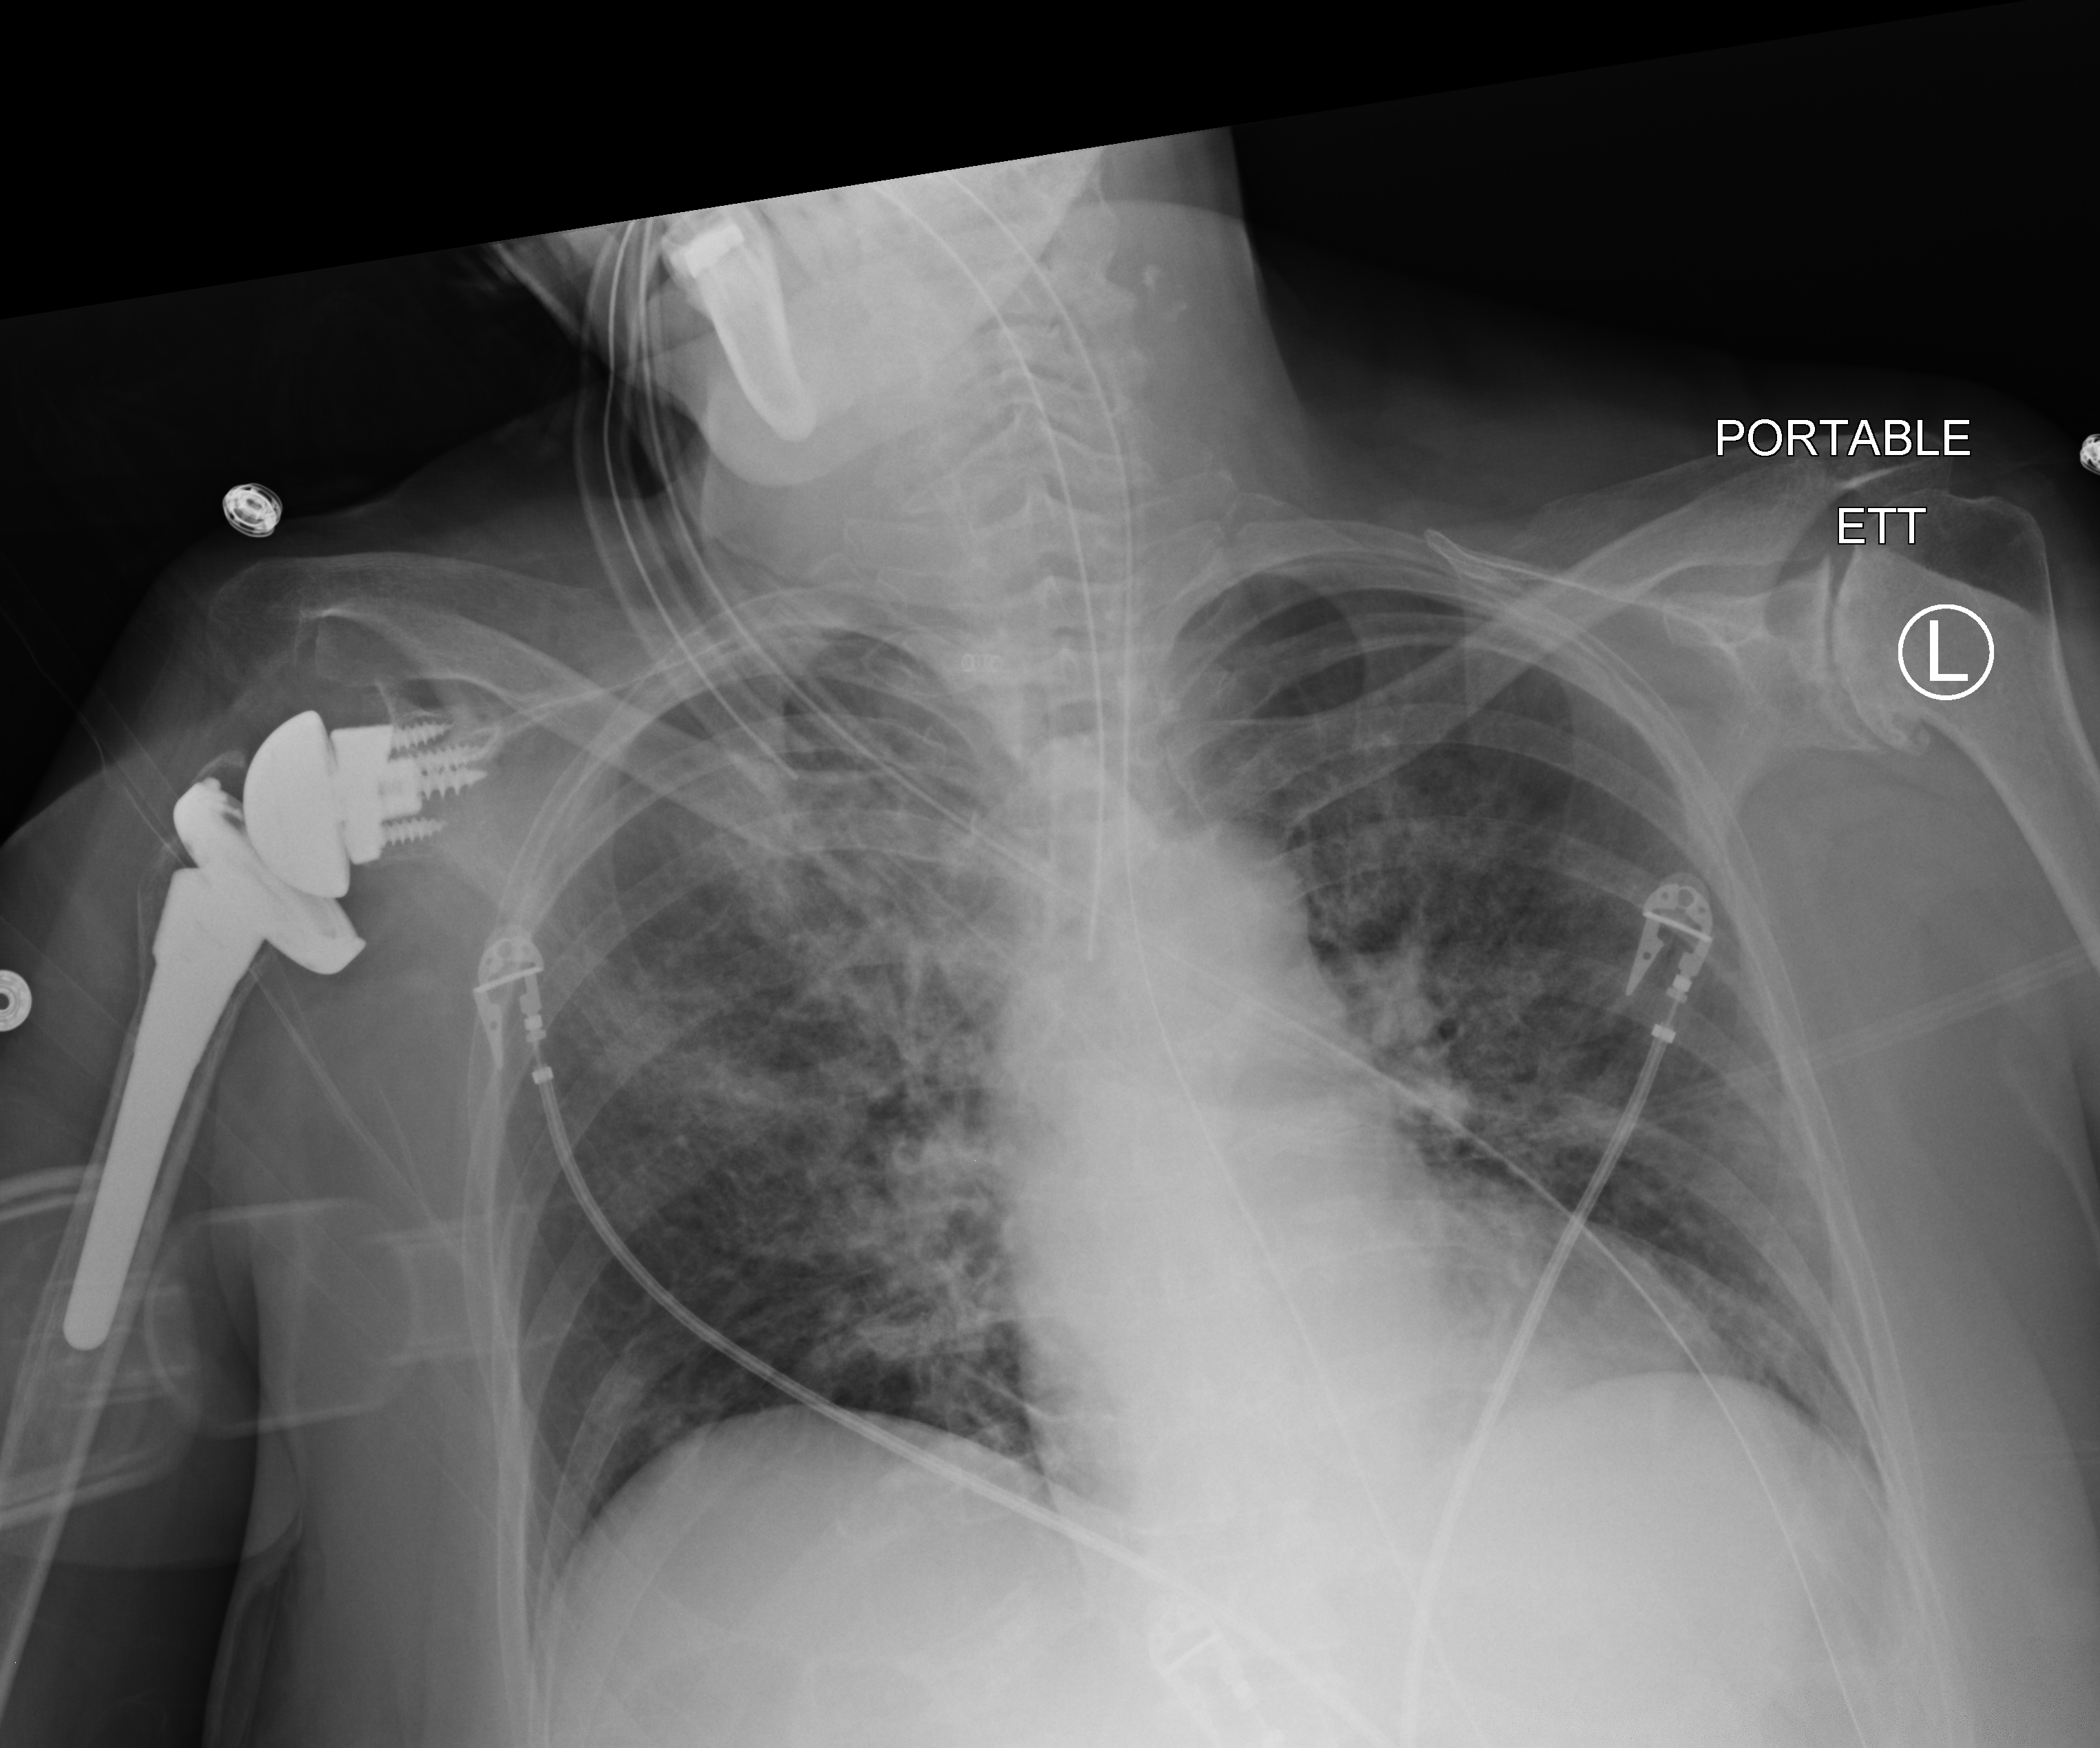
Bedside chest radiograph (computed radiography); anteroposterior (AP) projection. Female patient hospitalised with COVID-19, age 60–74 years.
Admission-level facts for this patient (not findings on this image; timing relative to this image not recorded): admitted to intensive care during this hospital stay: yes.